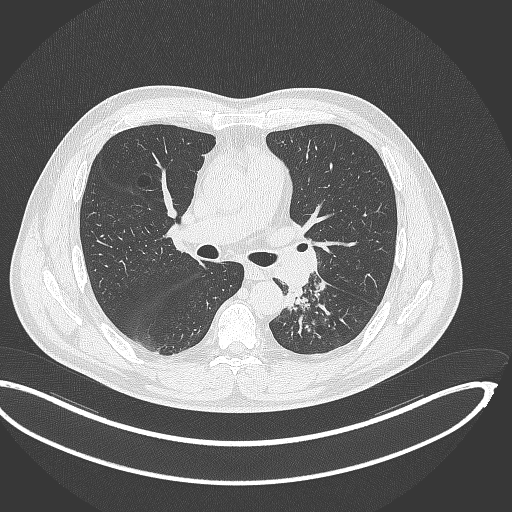
Chest CT, one axial slice. Position 209 of 362 along the scan axis. Reconstruction kernel B70f. 120 kVp. Lung window (W 1500 / L -600 HU). 1 mm slice thickness. 512 × 512 image matrix. Patient: male, 50 years. Case-level facts recorded for this patient, not image findings: clinical TNM (as recorded): T2a N3 M0.
Outlined on this slice (rectangle marked by the reading radiologist):
- lung tumour (recorded histology: squamous cell carcinoma): bounding box <281,285,309,310> (left, top, right, bottom; pixels)